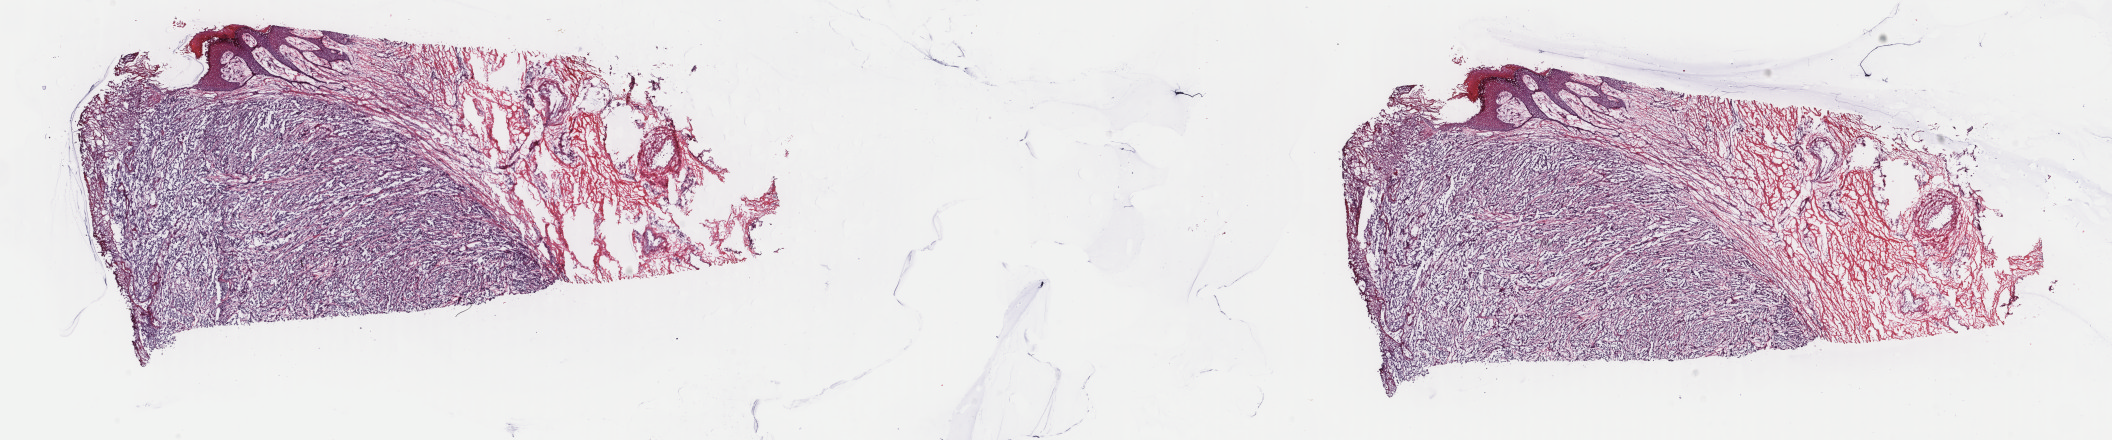
Digitized H&E-stained tissue section (whole slide), low-resolution overview of the scanned area, about 33.5 x 7.0 mm (slide scanned at 40x); frozen section from the top of the tissue portion; primary tumour sample from the skin. Patient: female, age at initial diagnosis 56 years. Composition of this section per pathologist review: tumour cells 65%, tumour nuclei 75%, normal cells 35%, stromal cells 0%, necrosis 0%. Infiltration values recorded for this section: lymphocyte infiltration 0%, monocyte infiltration 0%, neutrophil infiltration 0%.
Pathologic diagnosis: Malignant melanoma, NOS. AJCC pathologic stage: IIC (7th edition).